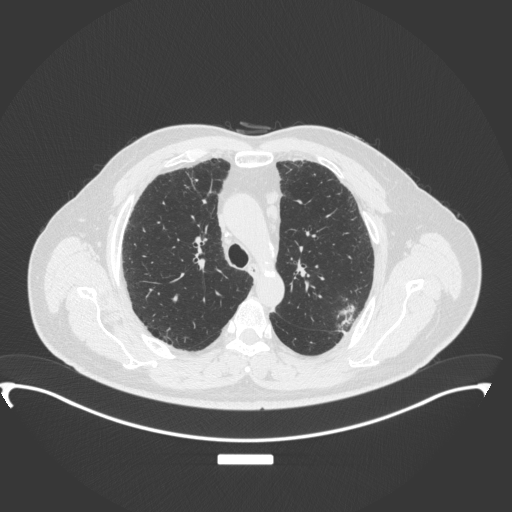
Chest CT, one axial slice. Position 255 of 350 along the scan axis. 120 kVp. Lung window (W 1500 / L -600 HU). 1 mm slice thickness. 512 × 512 image matrix. Male patient, age 64 years. From the clinical record (not read from this slice): clinical TNM (as recorded): T1c N1 M1.
Structures marked on this image (rectangle marked by the reading radiologist):
- lung tumour (recorded histology: adenocarcinoma): box from (x=332, y=302) to (x=358, y=338) px